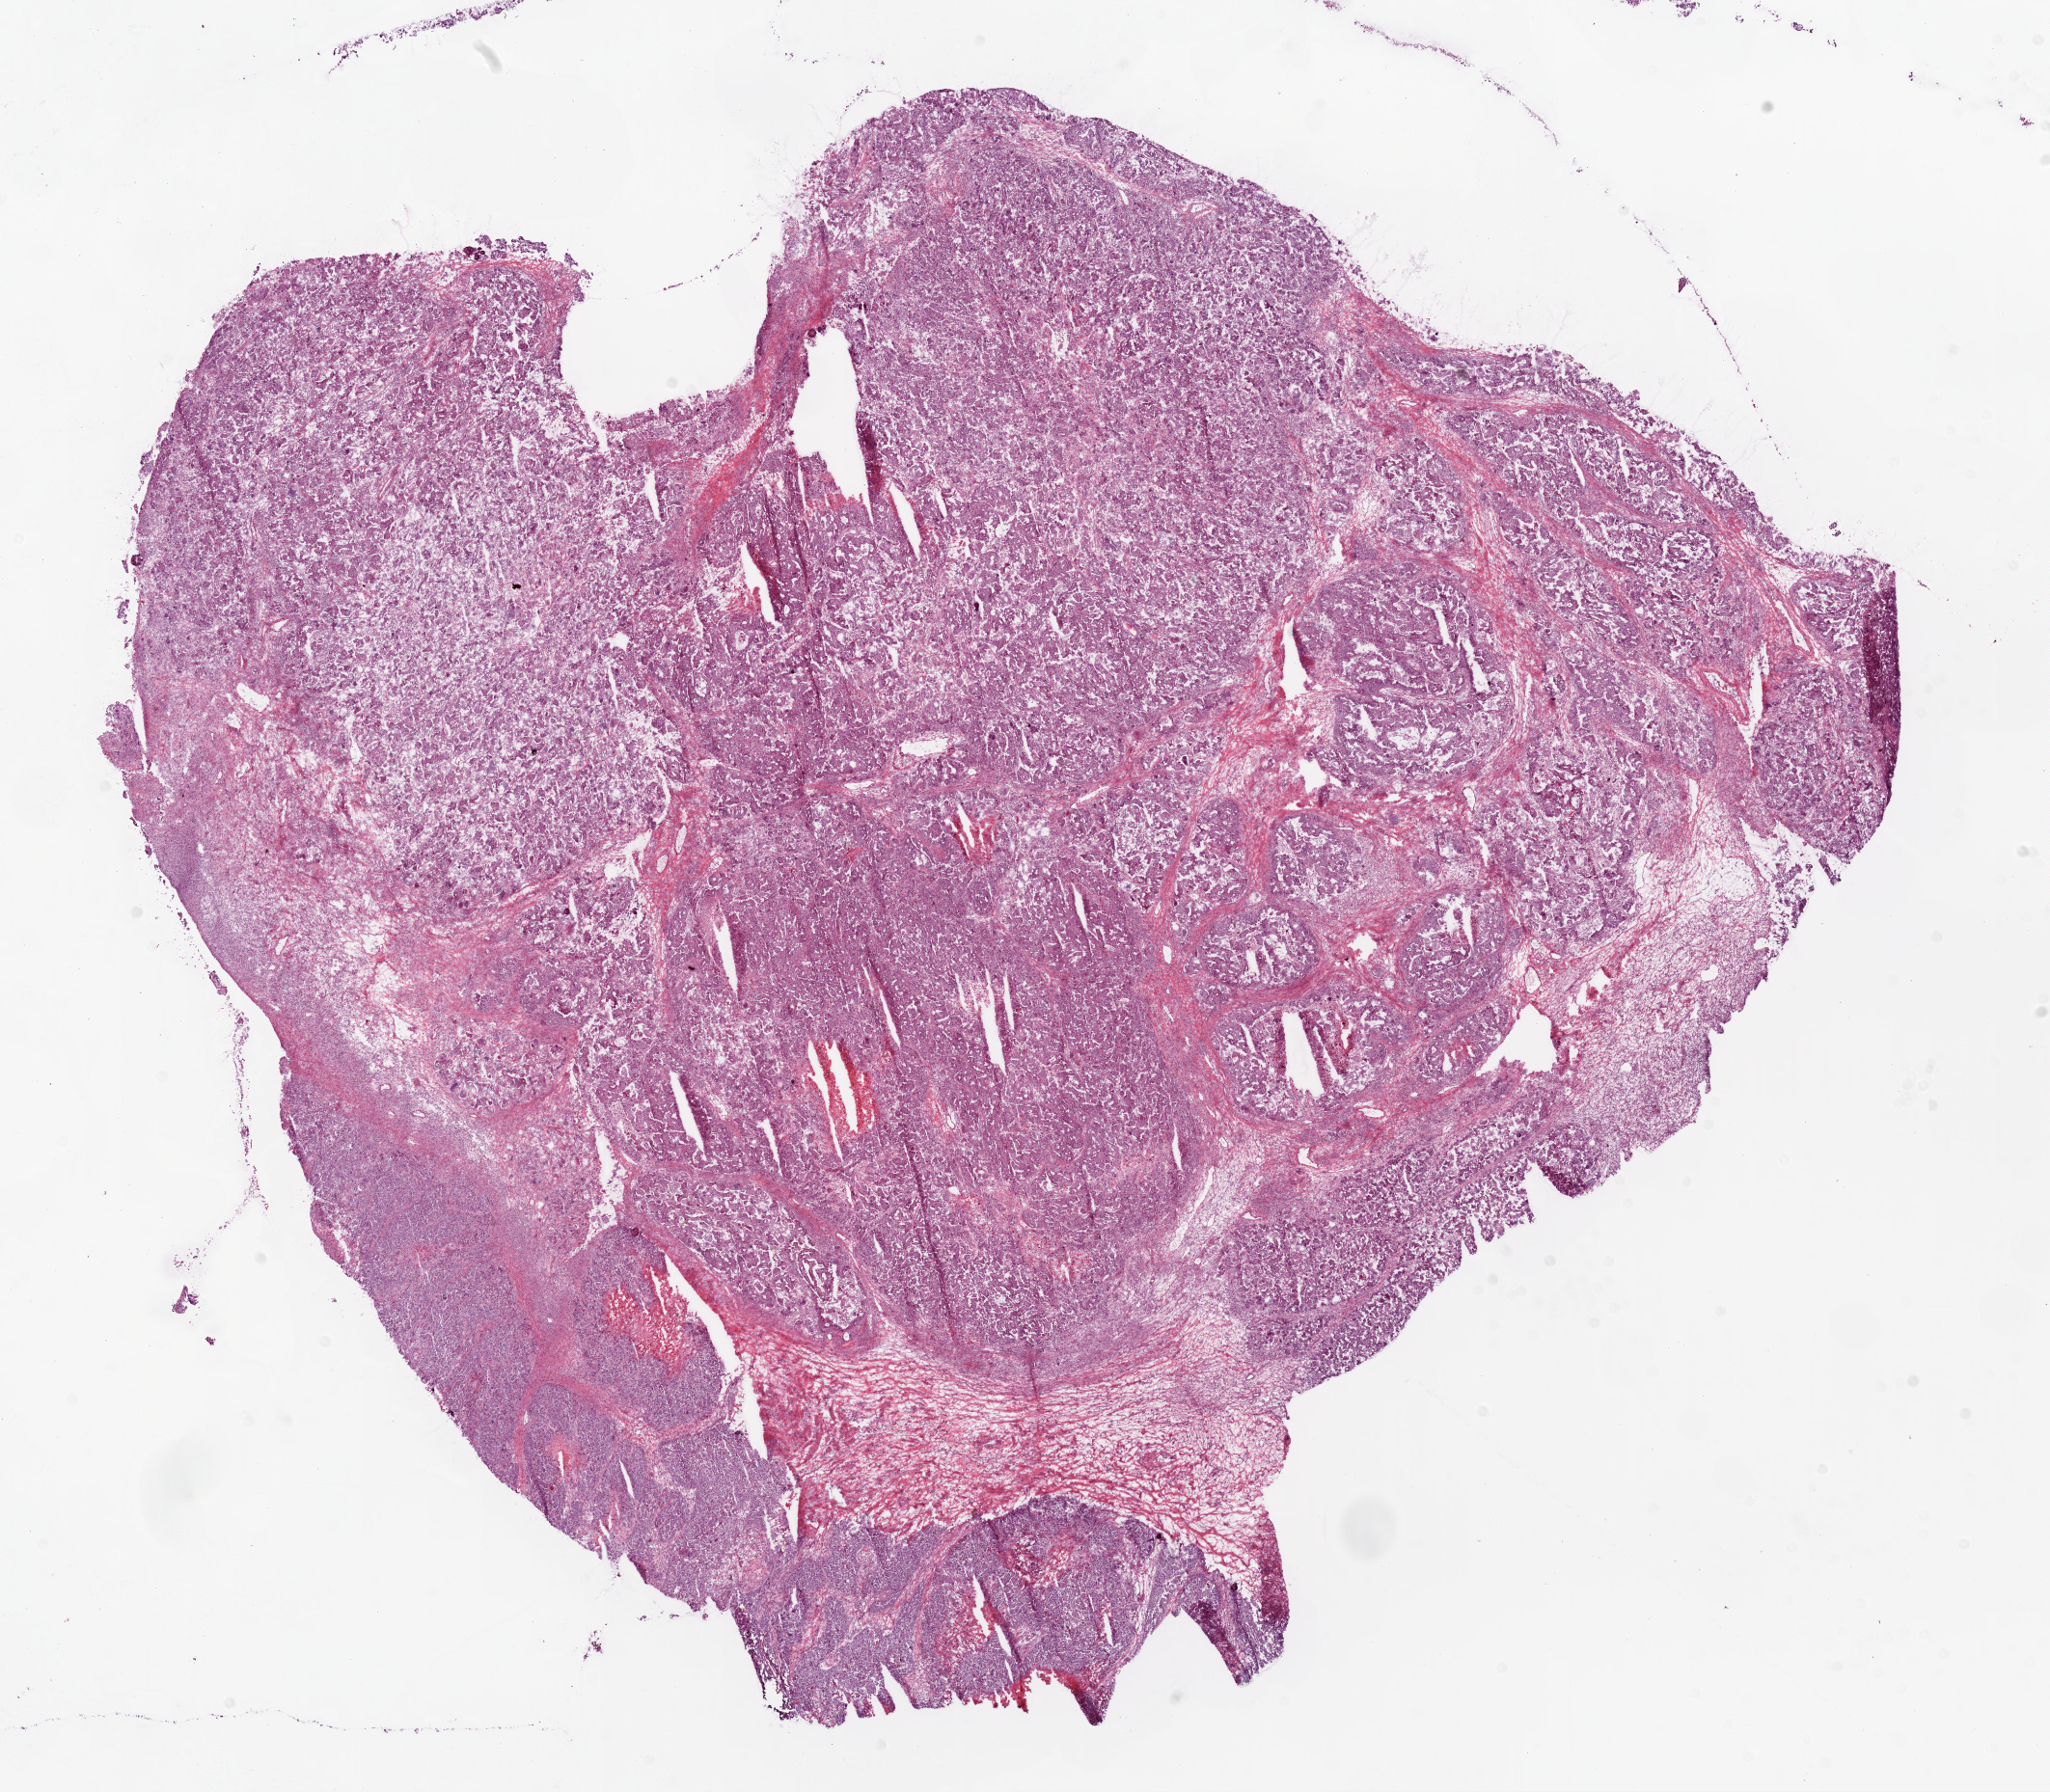
Hematoxylin and eosin (H&E) stained whole-slide image — shown as a low-resolution overview of the whole scanned area (about 17.1 x 14.9 mm), frozen section, primary tumour sample from the ovary. Patient: female, age at initial diagnosis 65 years. Histologic grade: G3 (poorly differentiated). Slide review estimates, as recorded: tumour cells 85%, tumour nuclei 90%, normal cells 0%, stromal cells 10%, necrosis 5%.
* FIGO stage: IIIC
* laterality: bilateral
* diagnosis: Serous cystadenocarcinoma, NOS